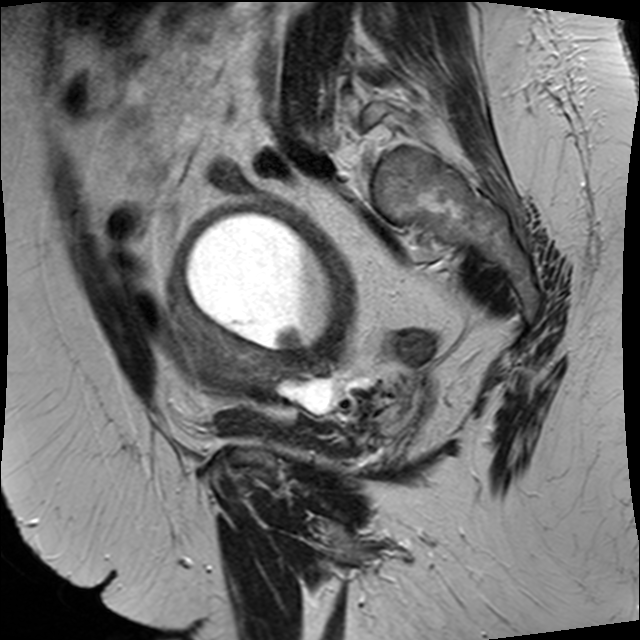
Pelvic MRI for cervical cancer, one sagittal slice. Position 24 of 34 along the scan axis. T2-weighted. 1.5 T. TE 89 ms, TR 3320 ms. 640 × 640 image matrix, field of view 260 × 260 mm. Patient: female, 50 years.
Outlined on this slice (manually delineated by an expert):
- uterus and cervix: bounding box (x1, y1, x2, y2) in pixels: (165, 193, 413, 428)